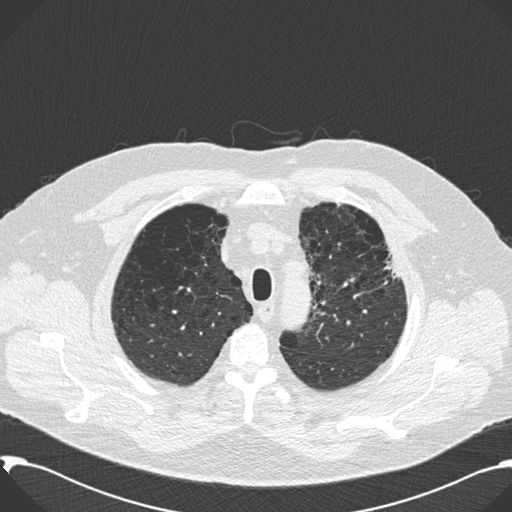
Low-dose screening chest CT, axial slice; second screening round (one year after baseline); lung window (W 1500 / L -600 HU); 2 mm slice thickness; standard (soft-tissue) reconstruction kernel (B30f). Male, age 59 years at enrolment. Current smoker at enrolment.
Lesion marked by an expert reader, bounding box [x1, y1, x2, y2] px = [366, 244, 409, 305]. Screening reader's record for this exam: no non-calcified nodule ≥4 mm recorded. Official screen result: negative screen, significant abnormalities not suspicious for lung cancer. Participant outcome: lung cancer diagnosed 518 days after this screen — bronchiolo-alveolar carcinoma, mixed mucinous and non-mucinous, left upper lobe, stage IA (AJCC 6th edition), 20 mm at pathology.